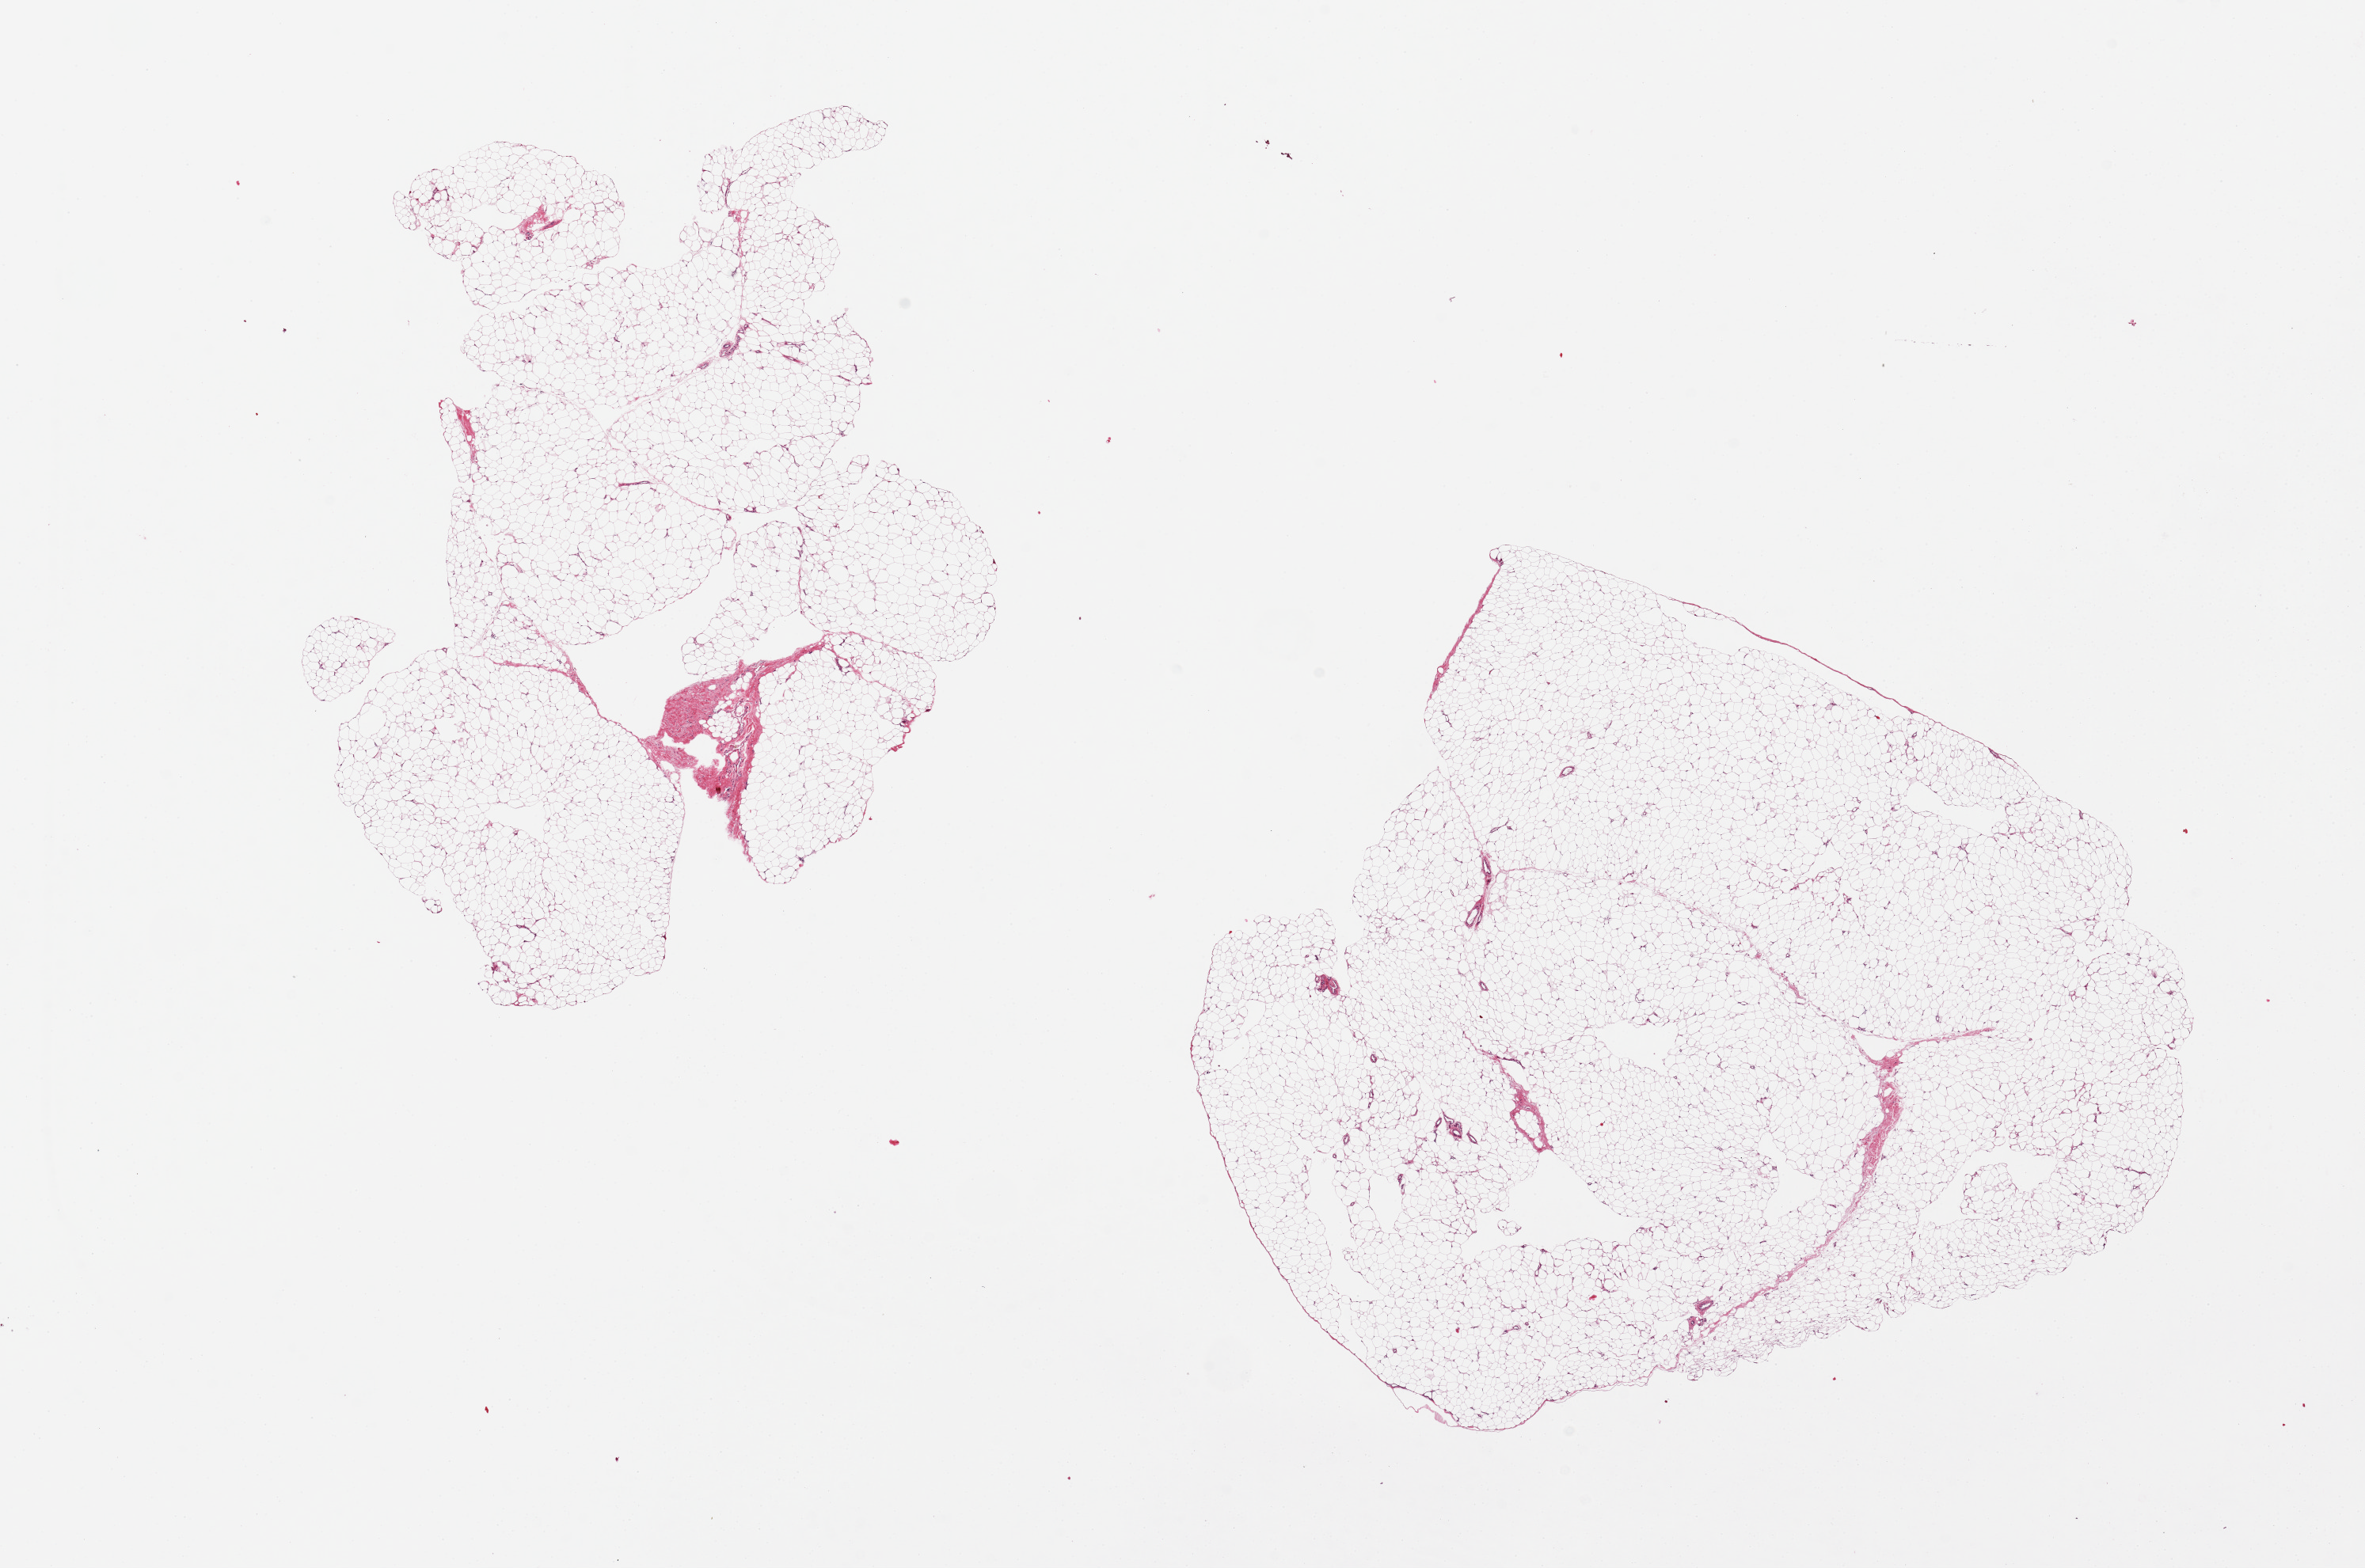
Hematoxylin and eosin (H&E) whole-slide image, low-resolution overview of the scanned area, about 23.6 x 15.7 mm; PAXgene-fixed, paraffin-embedded tissue; sampled site (target tissue): adipose tissue; tissue donor sample. Donor sex: female.
Pathologist's review note for this sample: 2 pieces; a few foci fibrous tissue/vessels.